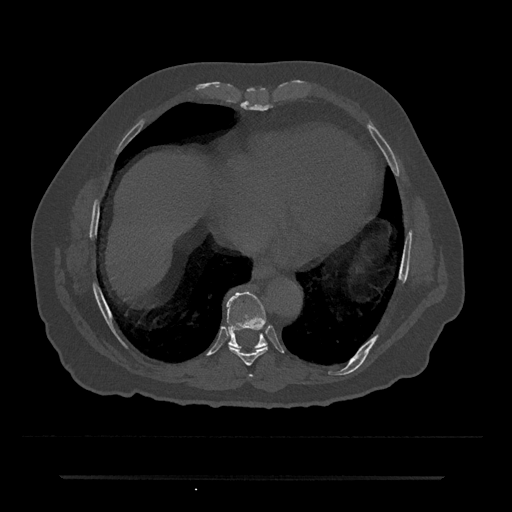
CT including the spine, one axial slice; position 309 of 797 along the scan axis; 120 kVp; bone window (W 1800 / L 400 HU); 0.5 mm slice thickness; 512 × 512 image matrix, field of view 437 × 437 mm. Patient: male, 69 years. Case-level facts recorded for this patient, not image findings: primary cancer: prostate.
Structures marked on this image (semi-automatic segmentation, software-assisted and operator-edited):
- T7 vertebra: box from (x=249, y=375) to (x=253, y=377) px
- T8 vertebra: (x=228, y=345)–(x=268, y=366)
- T9 vertebra: (x=227, y=291)–(x=267, y=349)